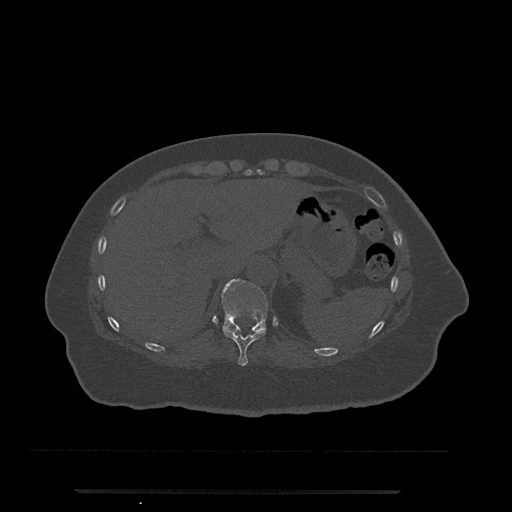
CT including the spine, one axial slice; position 258 of 797 along the scan axis; reconstruction kernel Br40s/3; 120 kVp; bone window (W 1800 / L 400 HU); 0.5 mm slice thickness; 512 × 512 image matrix, field of view 440 × 440 mm. Female patient, age 51 years. Case-level facts recorded for this patient, not image findings: primary cancer: neuro.
Outlined on this slice (semi-automatically segmented with operator editing):
- T10 vertebra: bounding box <223,328,266,366> (left, top, right, bottom; pixels)
- T11 vertebra: <222,279,268,333>